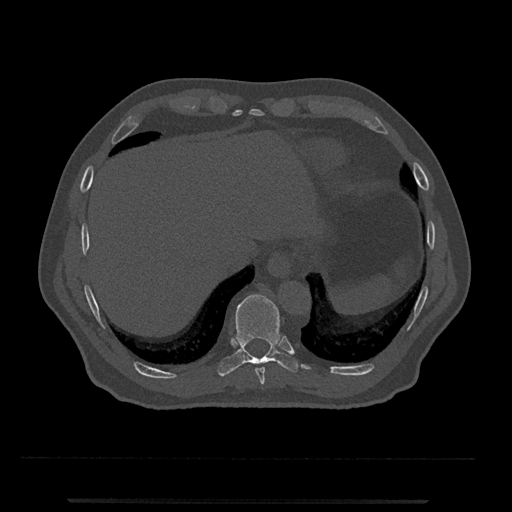
CT including the spine, one axial slice; slice 532 of 797 in the series (ordered by position); reconstruction kernel Br40s/3; 120 kVp; bone window (W 1800 / L 400 HU); 0.5 mm slice thickness; 512 × 512 image matrix, field of view 419 × 419 mm. Patient: male, 63 years. From the clinical record (not read from this slice): primary cancer: prostate.
Outlined on this slice (semi-automatically segmented with operator editing):
- T10 vertebra: bounding box <217,294,300,377> (left, top, right, bottom; pixels)
- T9 vertebra: <255,367,265,384>